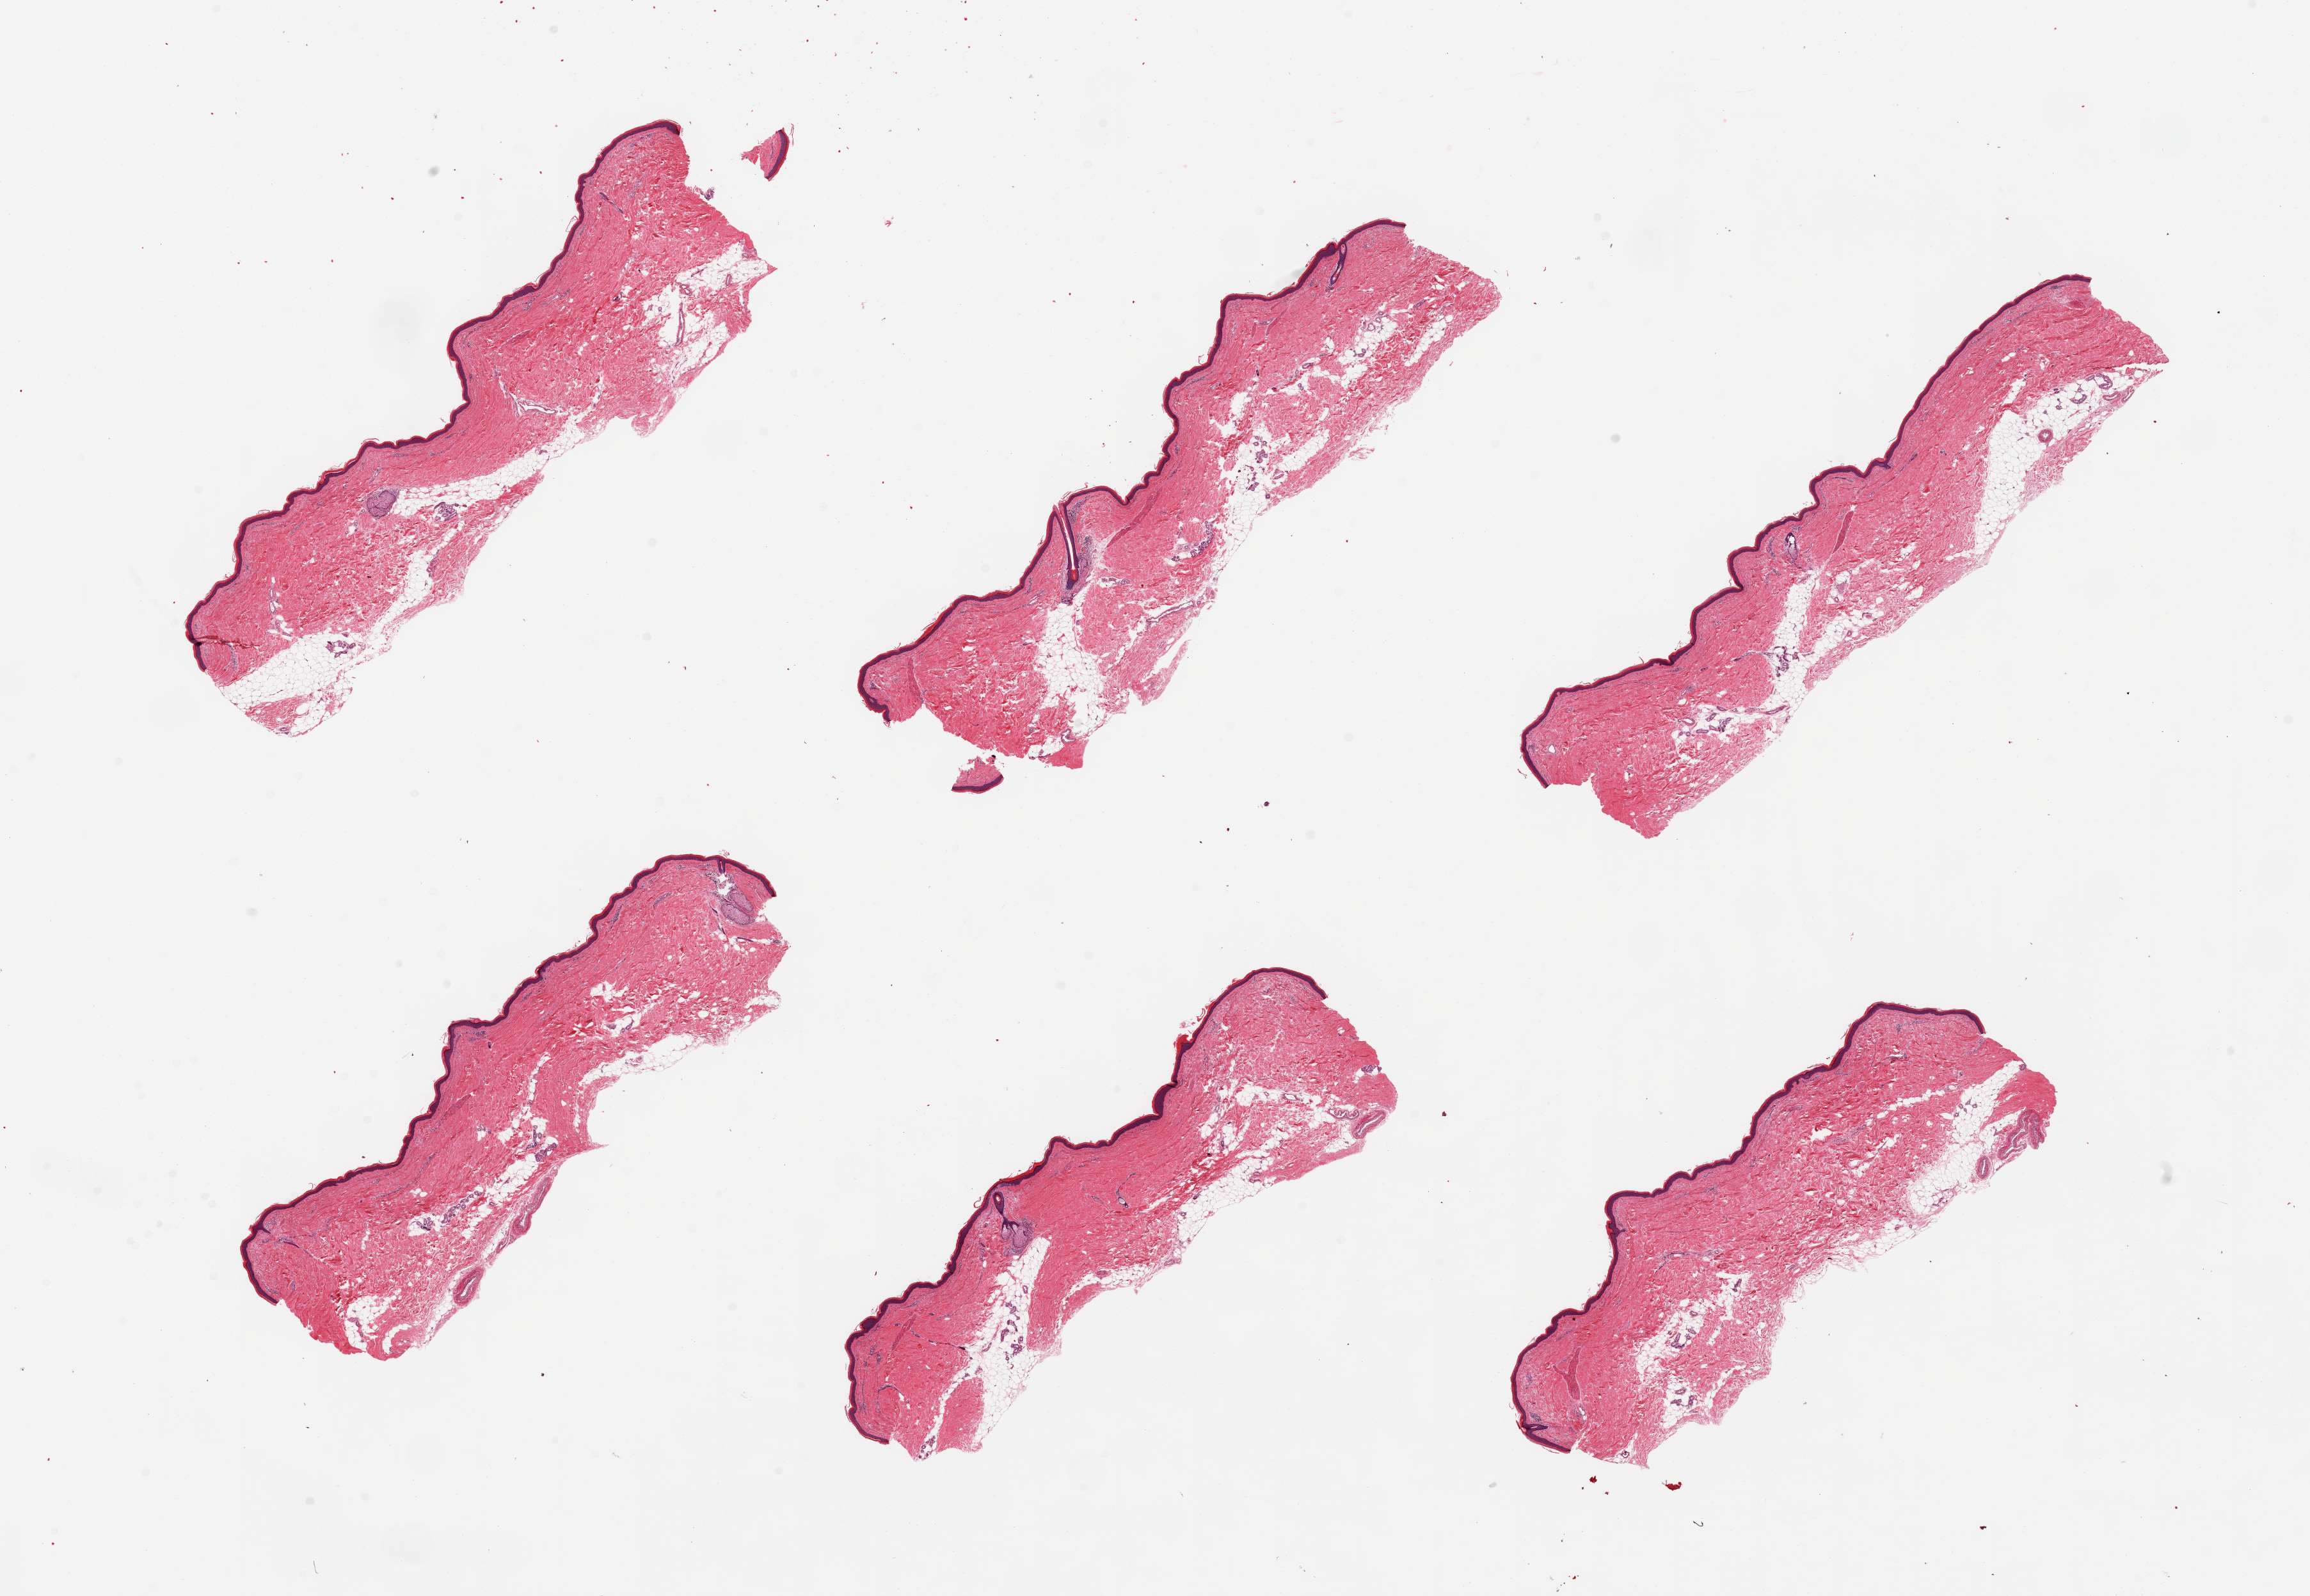
Haematoxylin and eosin whole-slide image, brightfield, shown as a low-resolution overview of the whole scanned area (about 28.5 x 19.7 mm, acquisition: 20x scan). PAXgene-fixed paraffin-embedded (PFPE) section. Sampled site (target tissue): skin of lower leg. Tissue donor sample. Donor sex: male.
Pathologist's review note for this sample: 6 pieces; well trimmed; 10-20% intradermal fat.